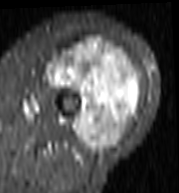
MRI of an extremity soft-tissue mass, one axial slice; STIR; MR volume resampled by the dataset authors to the PET/CT grid (not the native acquisition matrix); 3.27 mm slice thickness; 179 × 193 image matrix. Female patient. From the clinical record (not read from this slice): histological type: undifferentiated – high grade; grade: high; site of the primary tumour: left thigh.
Annotated regions visible in this slice (expert contour drawn on MRI and transferred to this co-registered scan by the dataset authors):
- gross tumour volume including surrounding oedema: bounding box [x1, y1, x2, y2] px = [47, 37, 142, 154]
- gross tumour volume (mass): [47, 37, 142, 154]